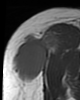
MRI of an extremity soft-tissue mass, one axial slice; MR volume resampled by the dataset authors to the PET/CT grid (not the native acquisition matrix); 80 × 100 image matrix, field of view 78 × 98 mm. Female patient. Case-level facts recorded for this patient, not image findings: histological type: synovial sarcoma; grade: intermediate; site of the primary tumour: right thigh.
Annotated regions visible in this slice (expert contour drawn on MRI and transferred to this co-registered scan by the dataset authors):
- gross tumour volume including surrounding oedema: bounding box [x1, y1, x2, y2] px = [12, 30, 61, 84]
- gross tumour volume (mass): [14, 30, 61, 82]